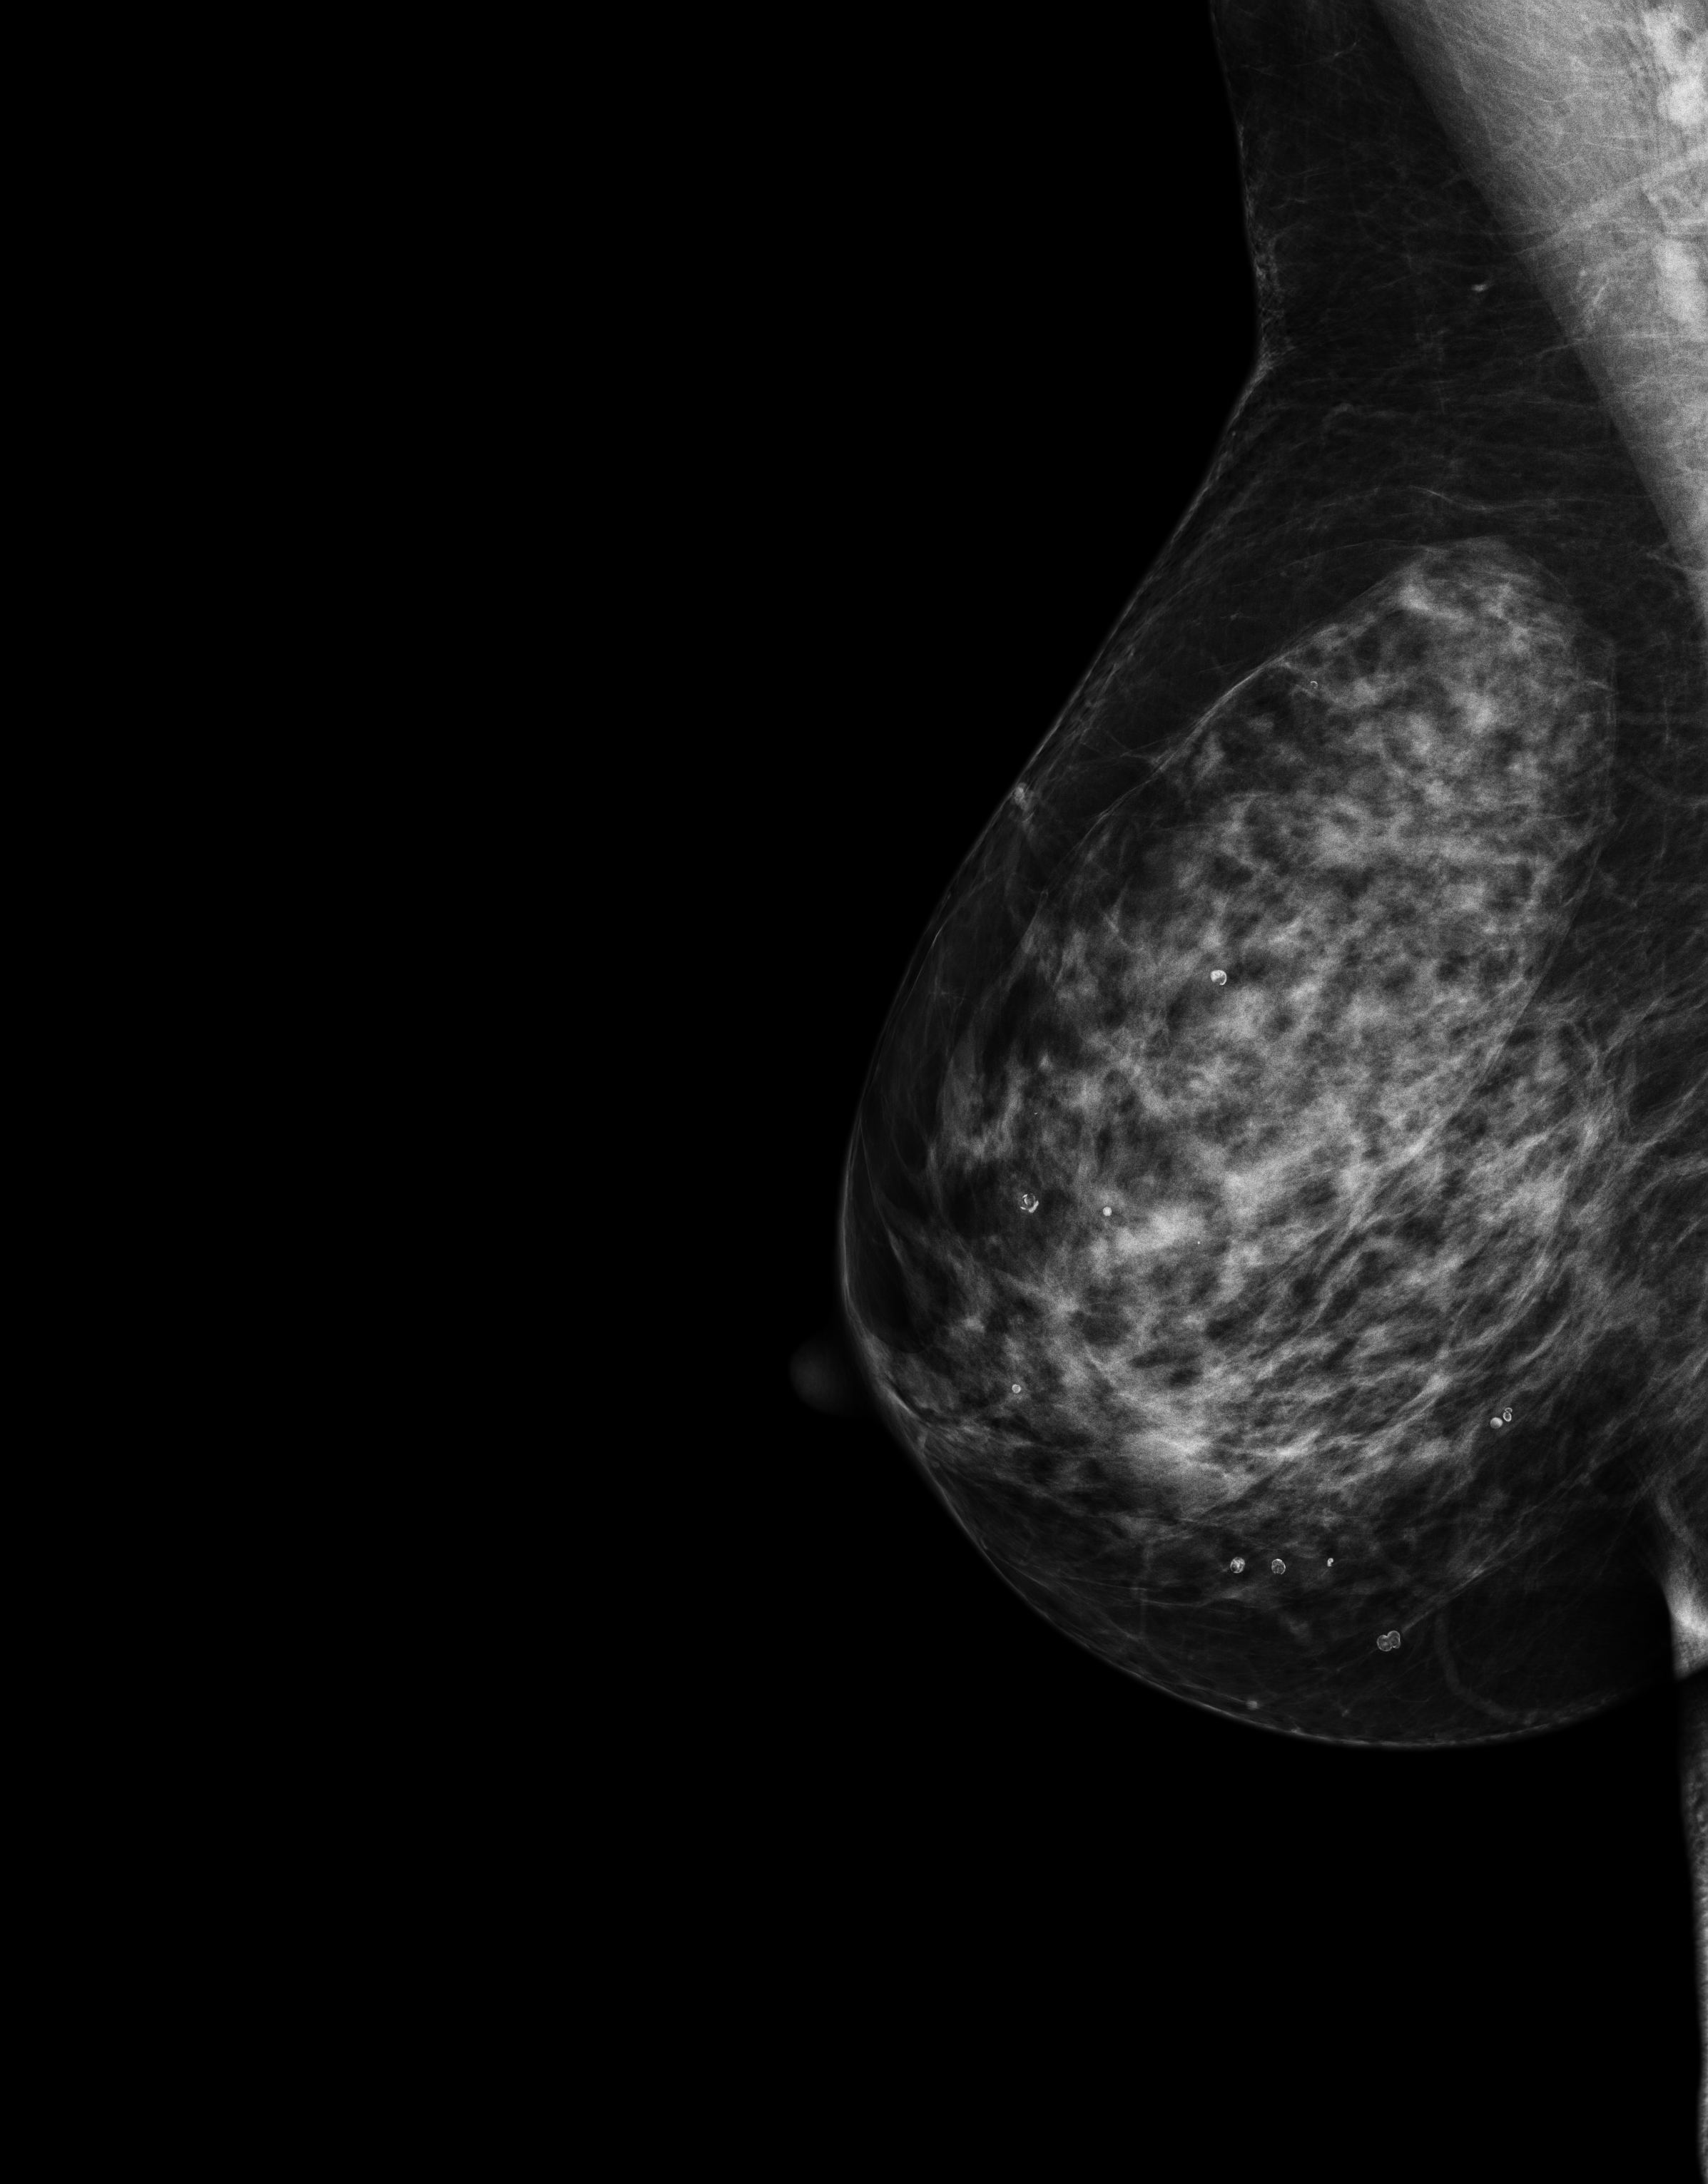
Digital mammogram (FFDM), right breast, mediolateral oblique (MLO) view, annual screening mammography examination, system: Senographe Essential ADS_56.21.3. Female patient, age 66 years.
Final BI-RADS category for the screening round (tomosynthesis exam, both breasts): category 1.